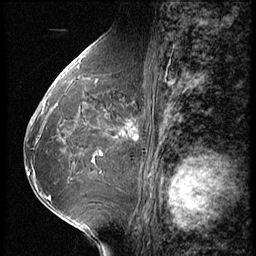
Breast MRI (dynamic contrast-enhanced), one sagittal slice. 3 images stored at this slice position (order not interpretable as contrast timing). 1.5 T. TE 4.2 ms, TR 9 ms. 256 × 256 image matrix. Patient: female, 65 years. Case-level facts recorded for this patient, not image findings: setting: breast cancer imaged before/during neoadjuvant chemotherapy; receptor status: HR-positive, HER2-negative.
Structures marked on this image (semi-automatically segmented with operator editing):
- analysis volume of interest (the breast-tissue region the enhancement analysis was run in; not a lesion): bounding box (x1, y1, x2, y2) in pixels: (104, 104, 154, 161)
- tumour enhancement mask (voxels above the 140 % enhancement threshold inside the analysis volume of interest): (123, 131, 126, 135)